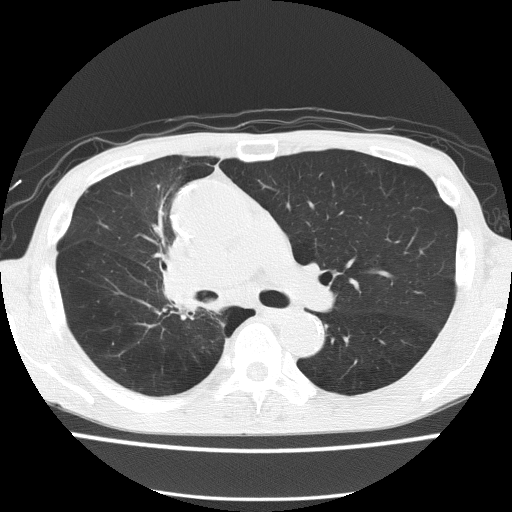
Chest CT (low-dose screening protocol), one axial image. First (baseline) screen. Lung window (W 1500 / L -600 HU). 512 × 512 image matrix, field of view 336 × 336 mm. Male, age 59 years at enrolment.
Expert-annotated lung lesion, box from (x=143, y=229) to (x=231, y=320) px. The screening reader recorded 5 non-calcified nodules or masses ≥4 mm on this exam; which of them this box marks is not recorded. Later outcome: lung cancer diagnosed 72 days after this screen — squamous cell carcinoma, NOS, right upper lobe, moderately differentiated (G2), stage IV (AJCC 6th edition).